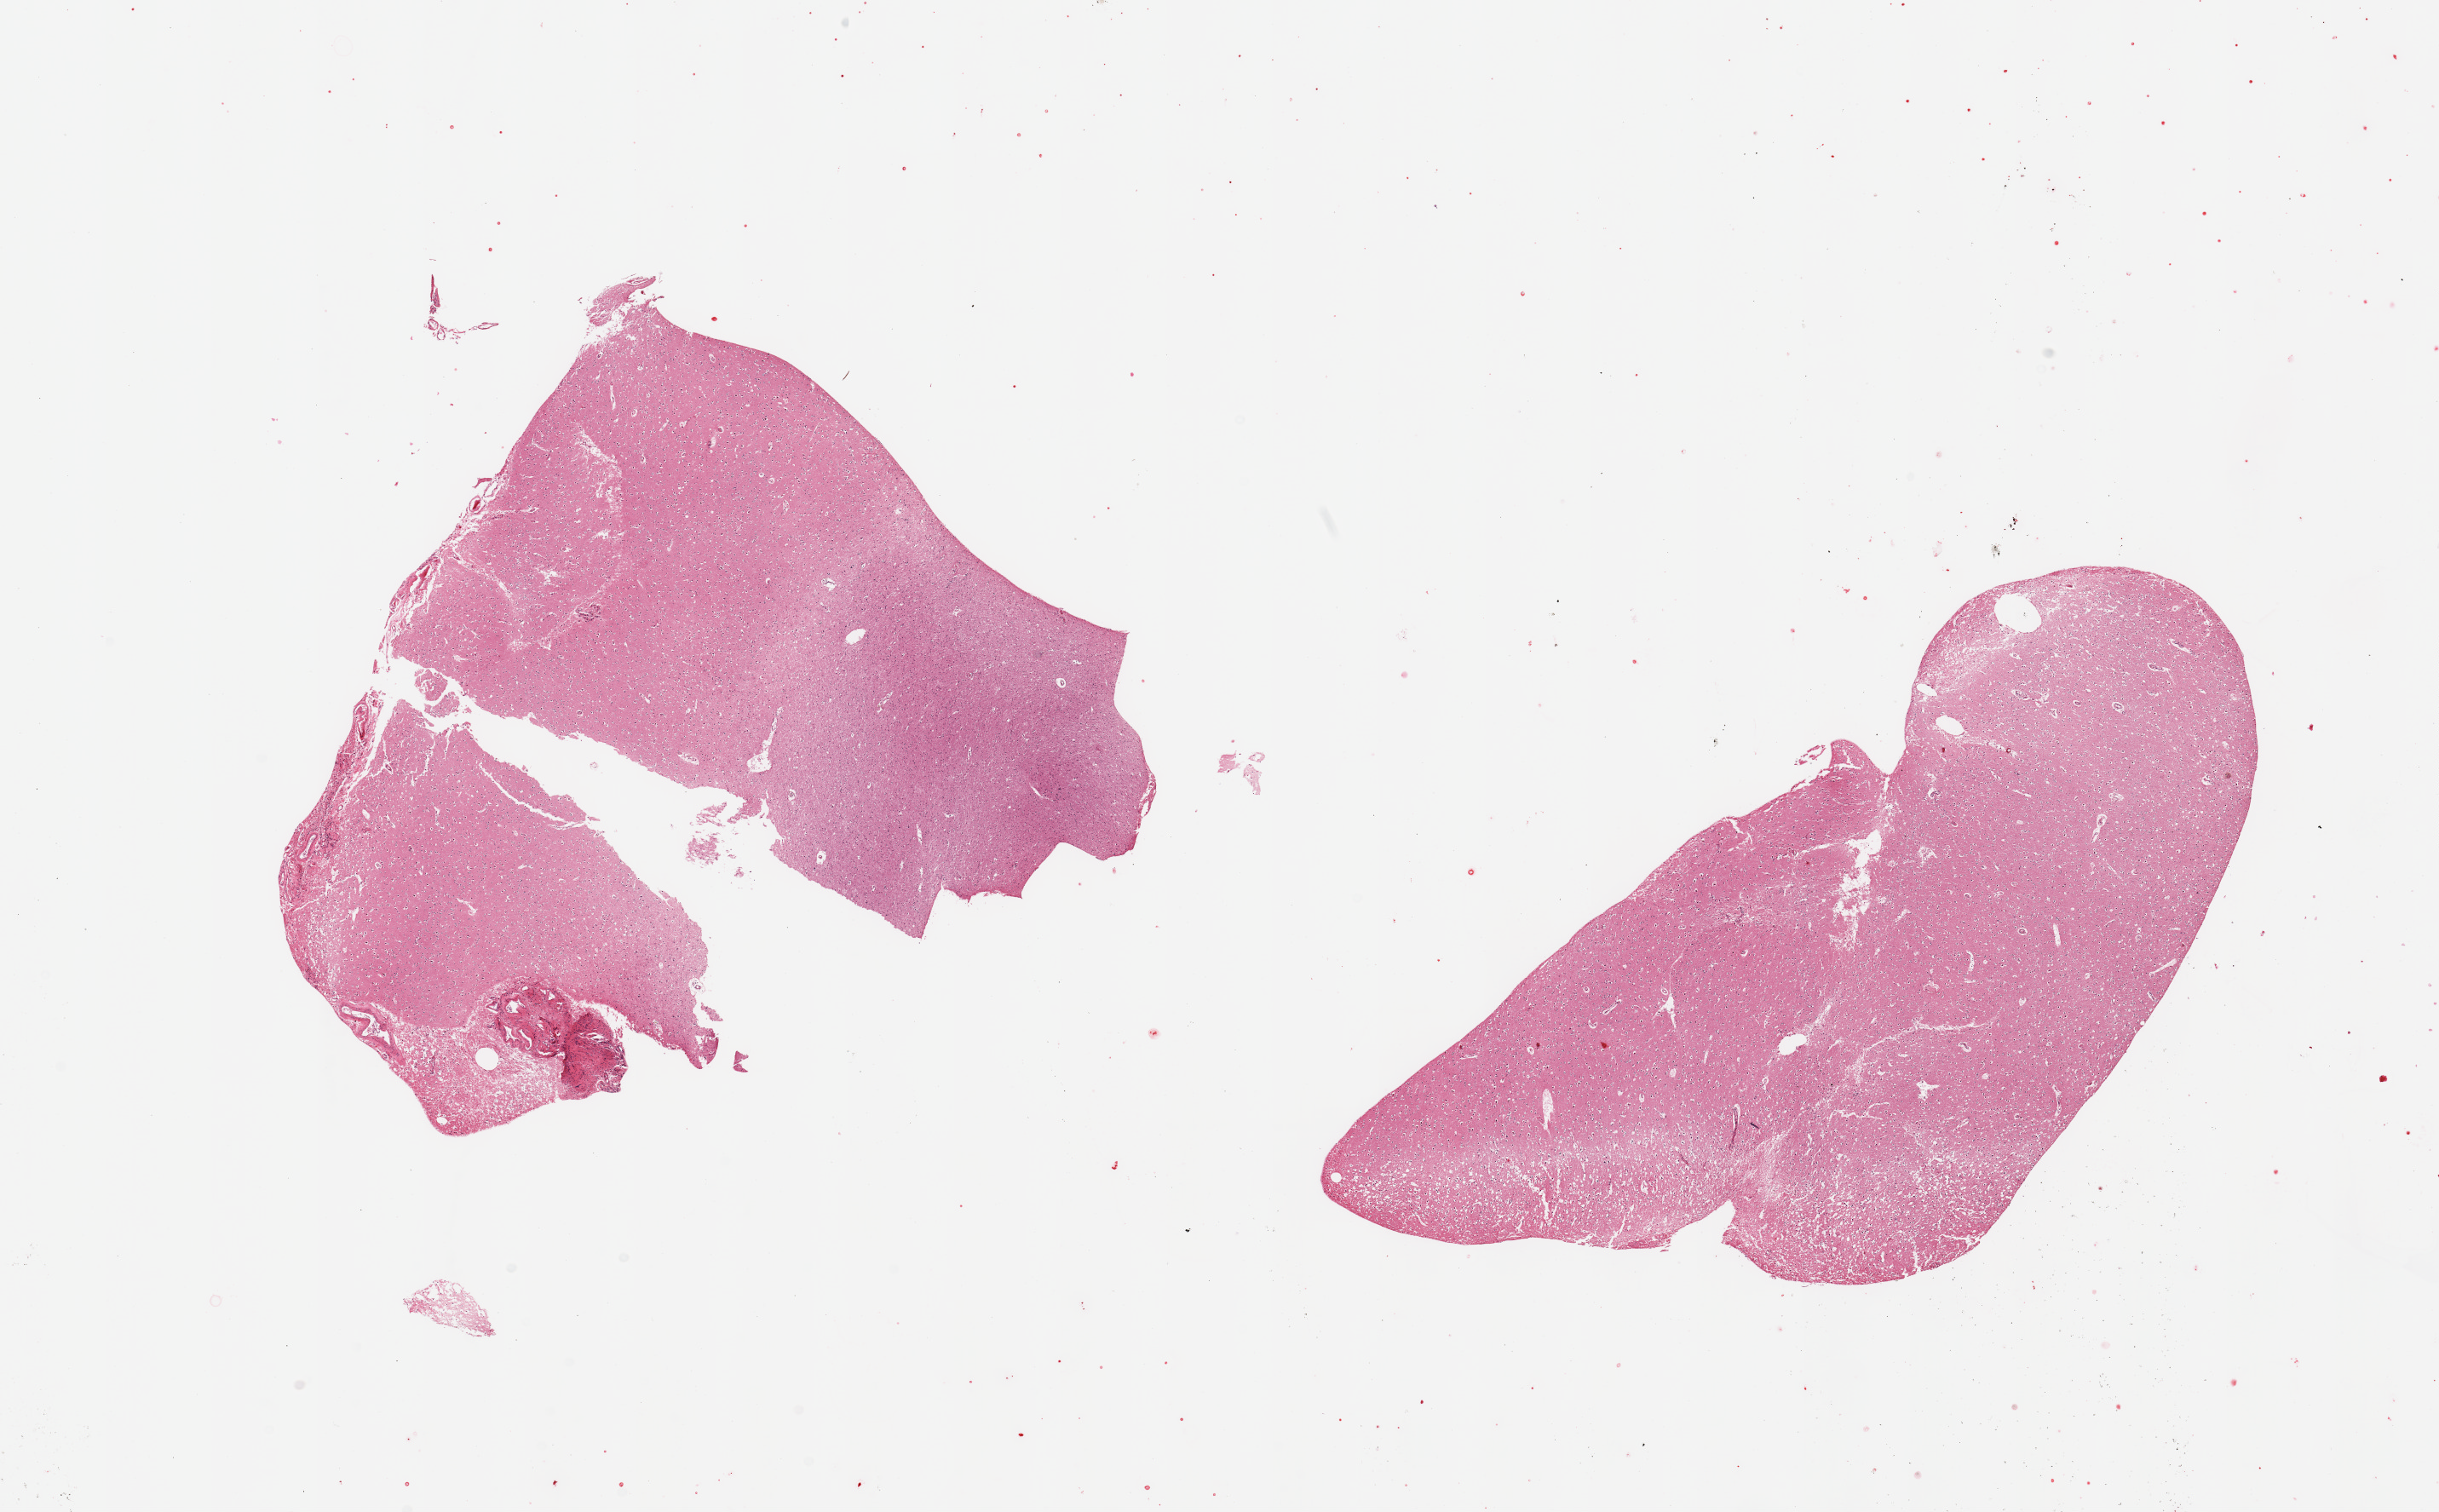
Whole-slide image, hematoxylin and eosin (H&E) stain, a low-resolution overview of the entire scanned area, about 22.6 x 14.0 mm; PAXgene-fixed, paraffin-embedded tissue; target tissue: cerebral cortex; donor tissue sample. Donor: male.
Pathologist's review note for this sample: 2 pieces.